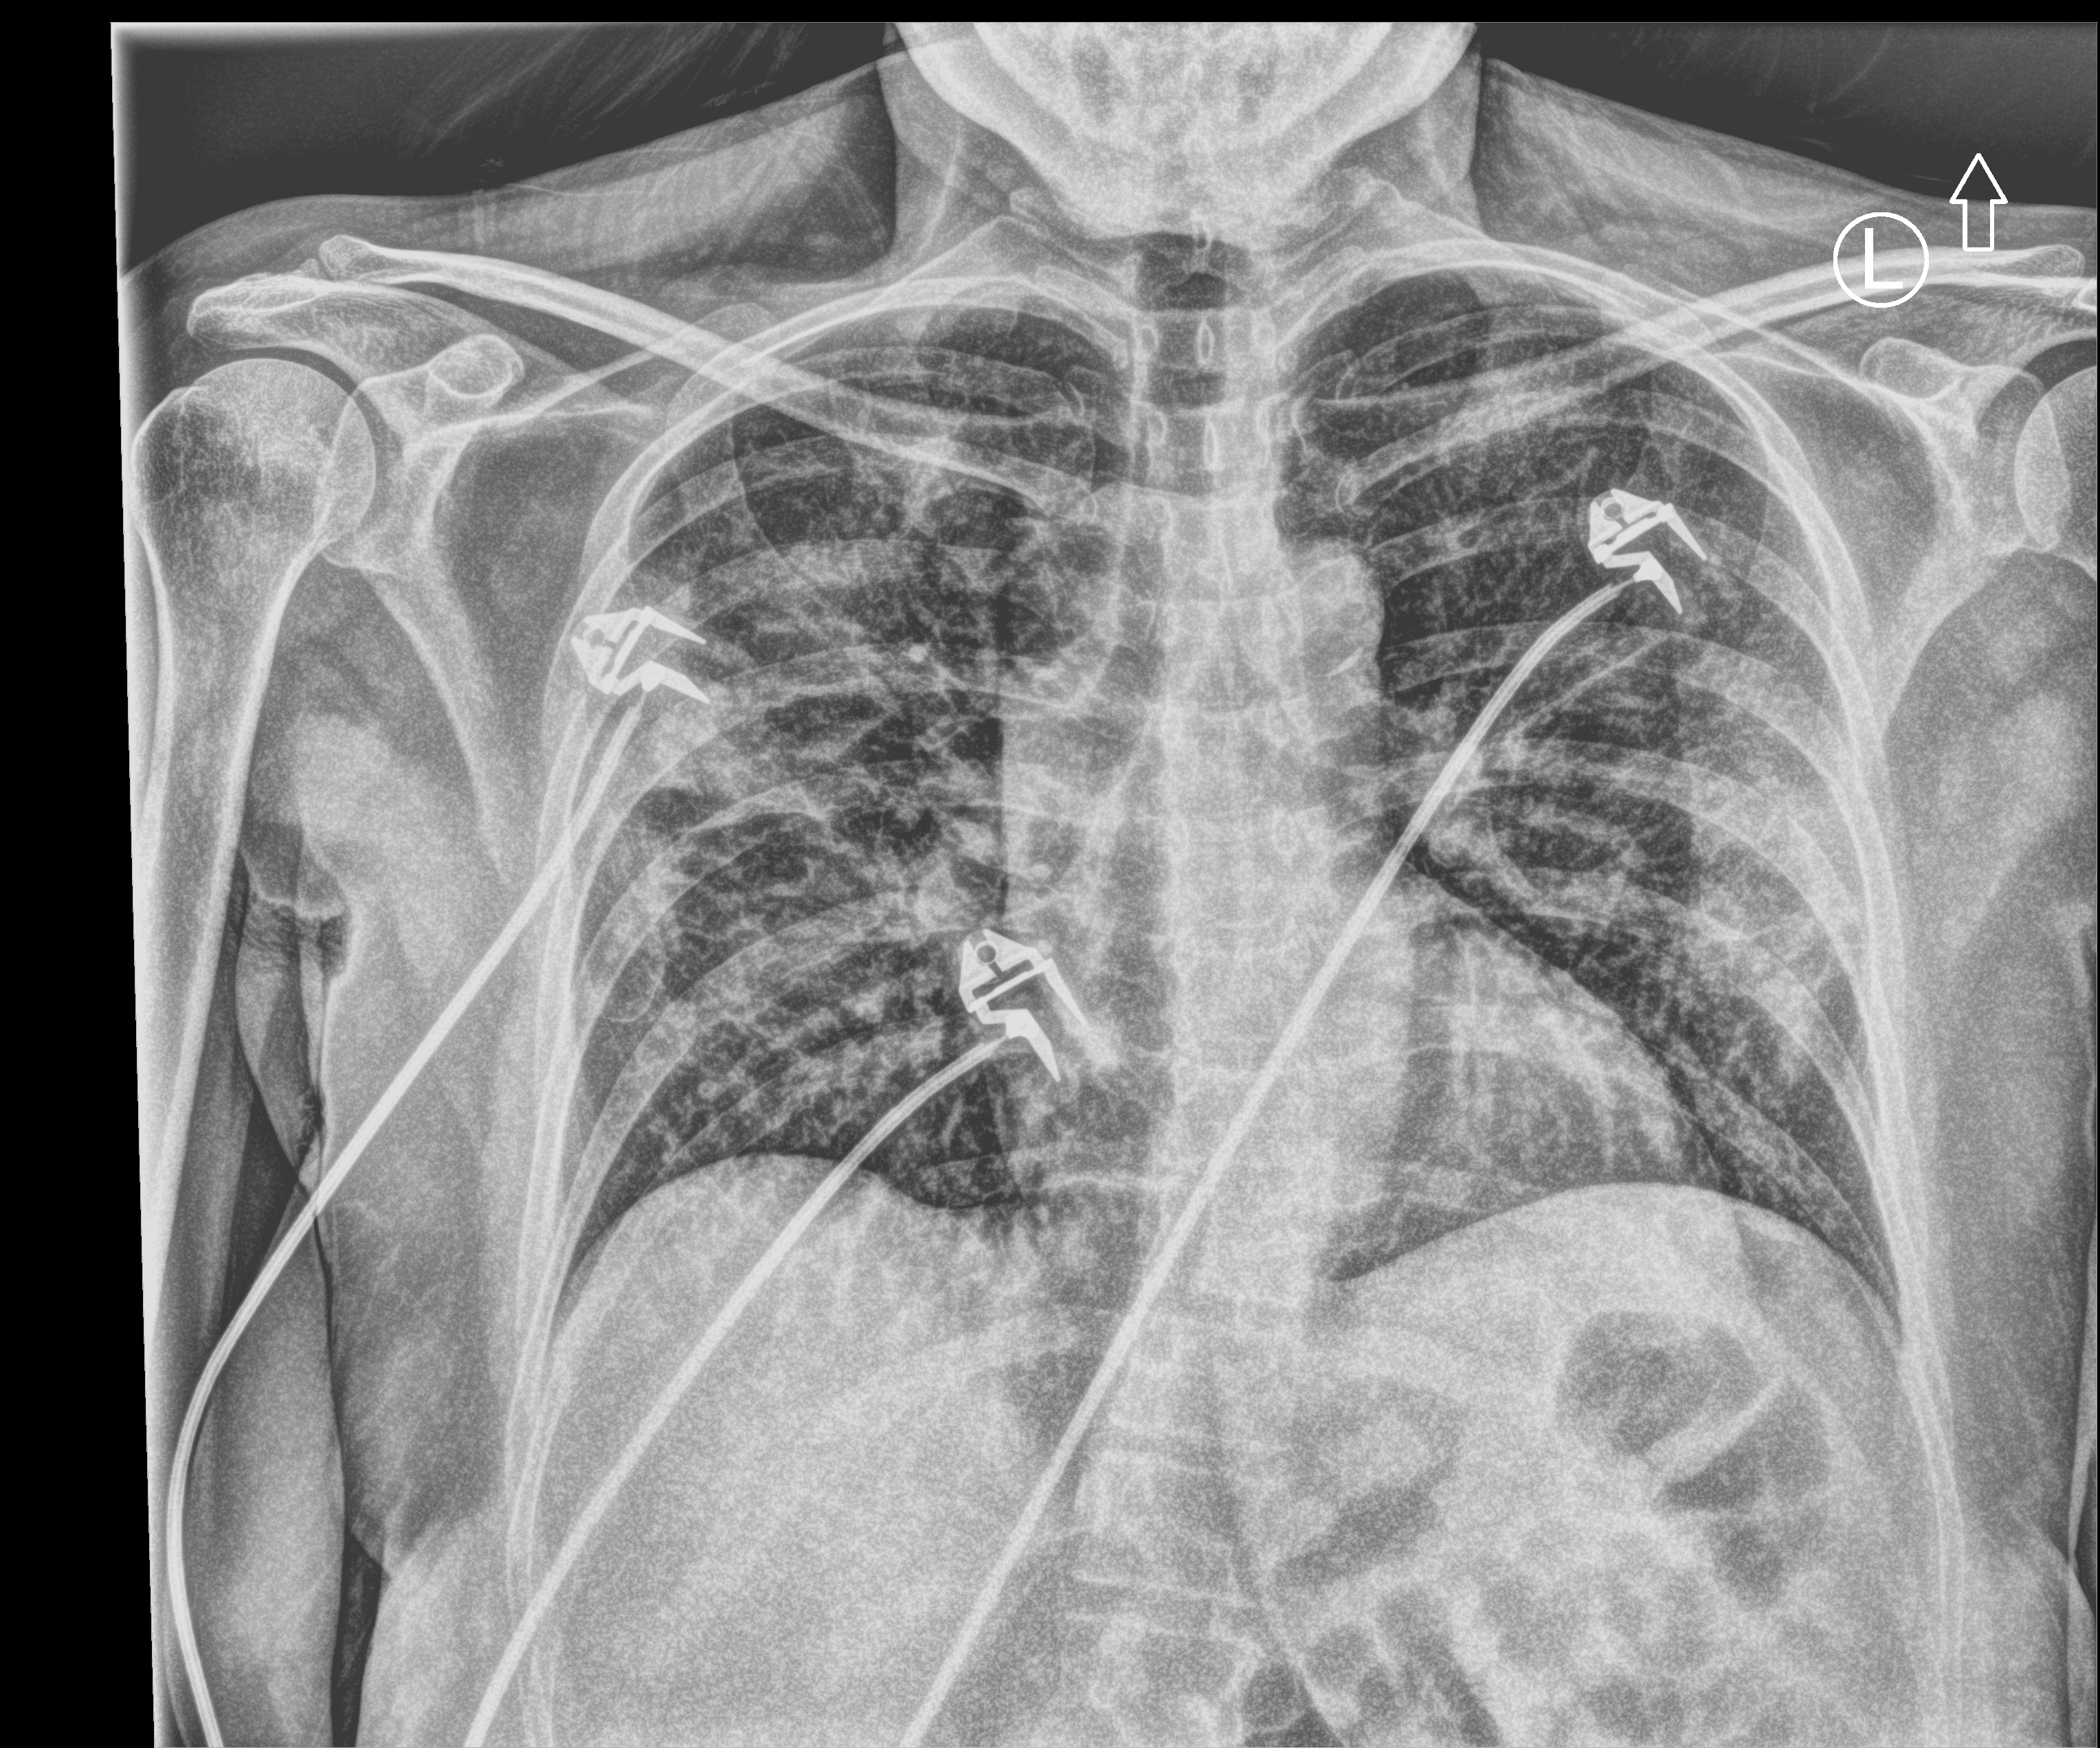
Bedside chest radiograph (computed radiography); anteroposterior (AP) projection. Female patient hospitalised with COVID-19, age 18–59 years.
Admission-level facts for this patient (not findings on this image; timing relative to this image not recorded): length of hospital stay: 15 days.